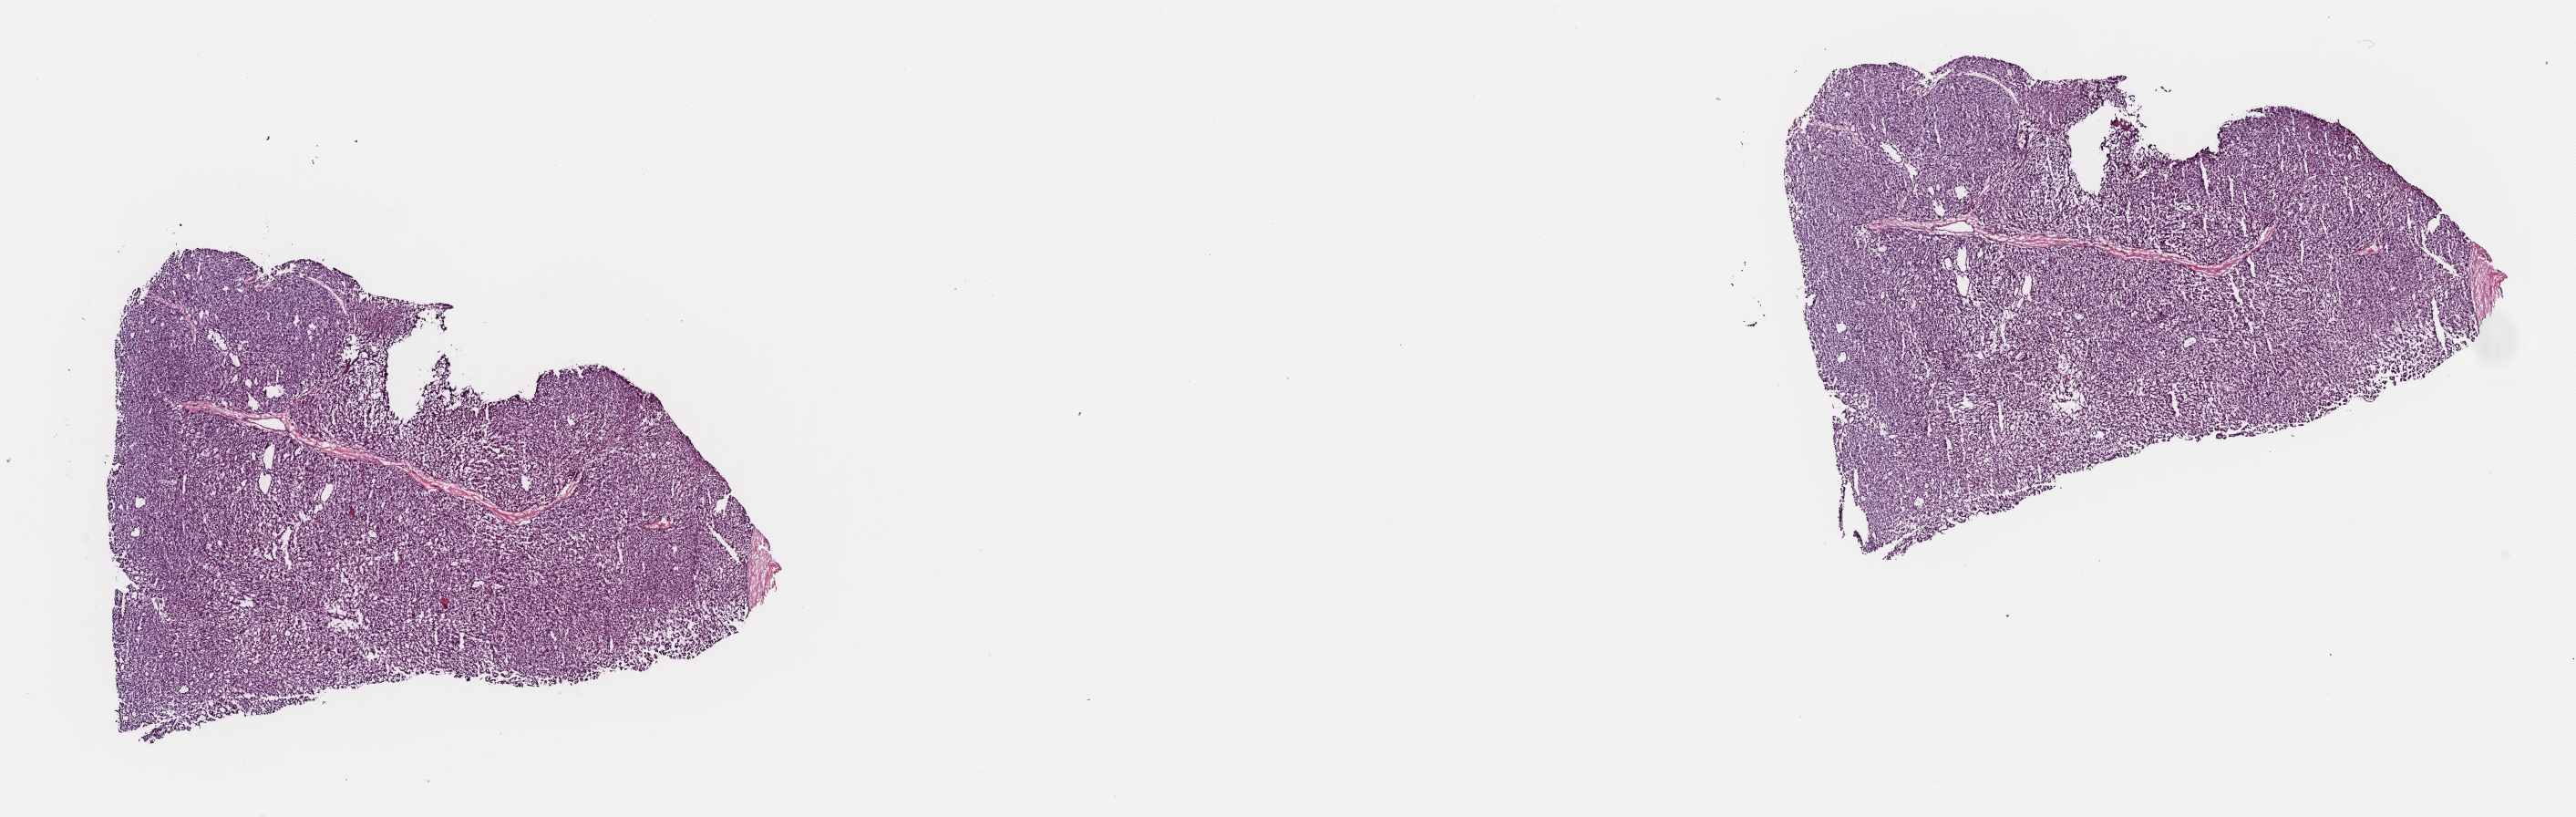
Digitized H&E-stained tissue section (whole slide) — a low-resolution overview of the entire scanned area, about 22.3 x 7.1 mm. Frozen section from the top of the tissue portion. Primary tumour sample from the liver. Male, age 77 years at initial diagnosis. Pathologist review of this section (percent, as recorded): tumour cells 83%, tumour nuclei 90%, normal cells 0%, stromal cells 5%, necrosis 12%. Infiltration values recorded for this section: lymphocyte infiltration 4%, monocyte infiltration 2%, neutrophil infiltration 0%.
Histologic diagnosis: Hepatocellular carcinoma, NOS.